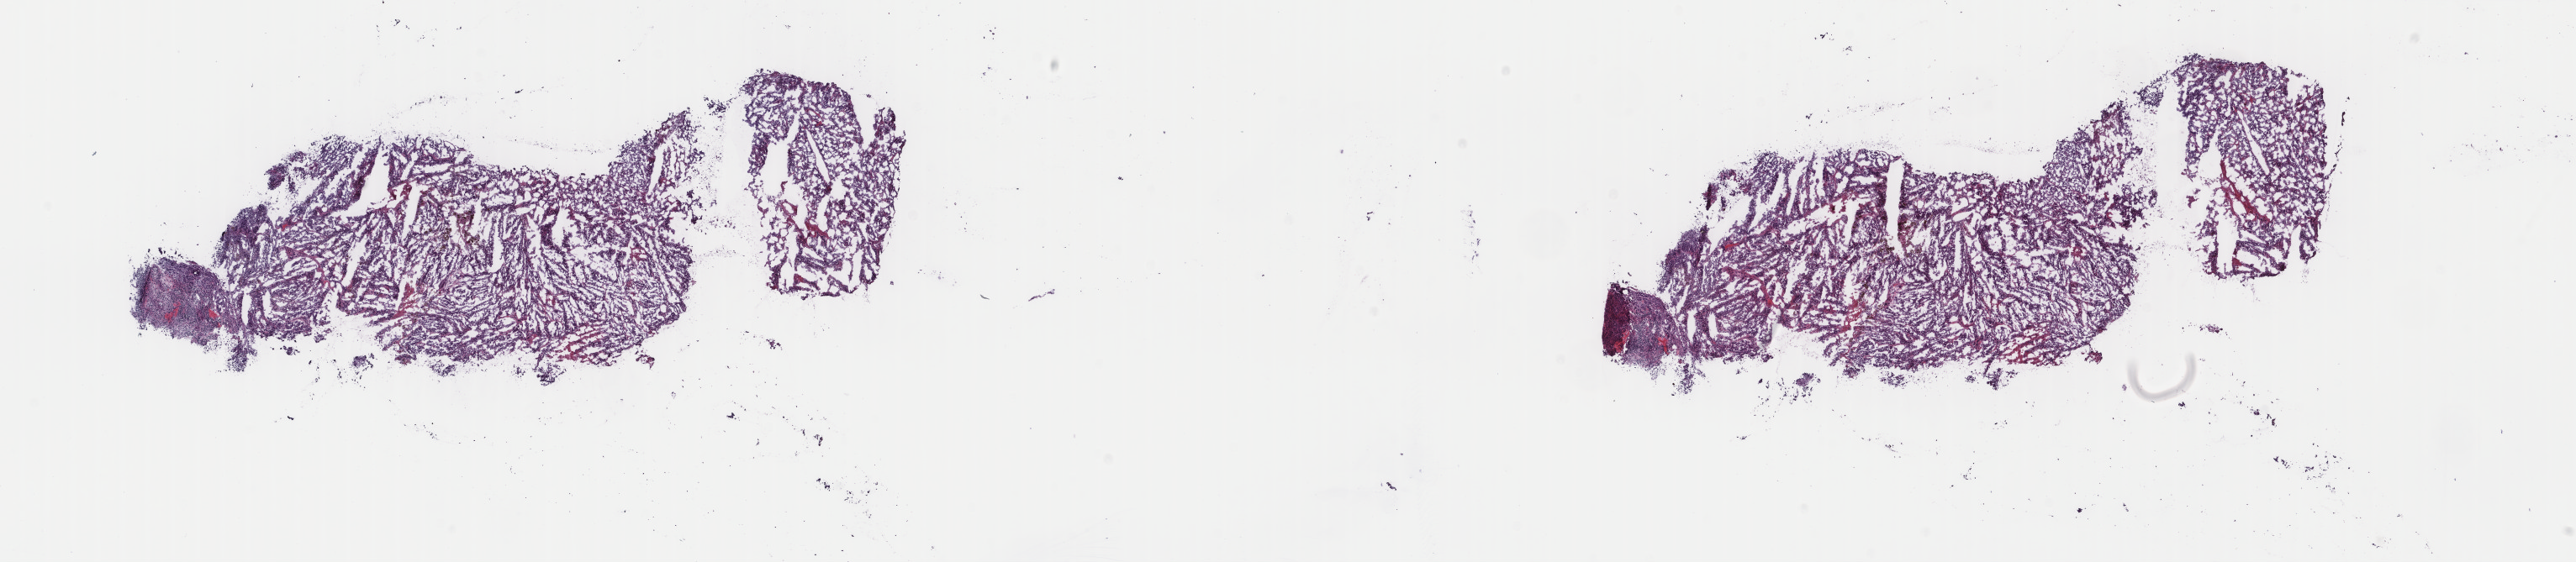
Whole-slide histology image, H&E, whole scanned area (about 24.3 x 5.3 mm) shown as a low-resolution overview, frozen section, metastatic tumour sample. Patient: female, age at initial diagnosis 56 years. Slide review estimates, as recorded: tumour cells 84%, tumour nuclei 85%, normal cells 0%, stromal cells 1%, necrosis 15%. Infiltration values recorded for this section: lymphocyte infiltration 15%, monocyte infiltration 0%, neutrophil infiltration 0%.
* this section: metastatic tumour tissue
* patient diagnosis: Malignant melanoma, NOS